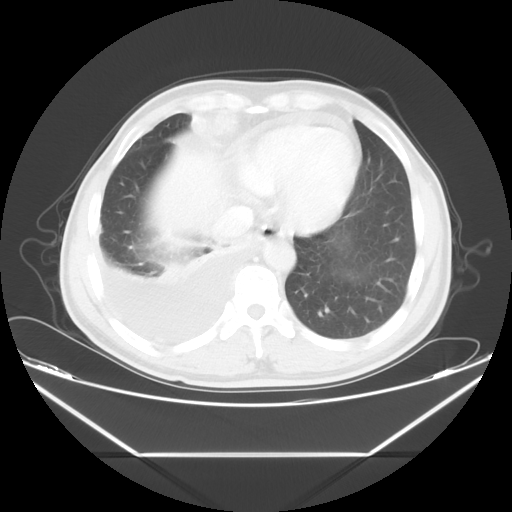
Chest CT, one axial slice. Position 14 of 56 along the scan axis. Reconstruction kernel STANDARD. 120 kVp. Lung window (W 1500 / L -600 HU). 512 × 512 image matrix. Patient: male, 57 years. Case-level facts recorded for this patient, not image findings: clinical TNM (as recorded): T2 N3 M1.
Outlined on this slice (rectangle marked by the reading radiologist):
- lung tumour (recorded histology: adenocarcinoma): bounding box <184,99,243,153> (left, top, right, bottom; pixels)